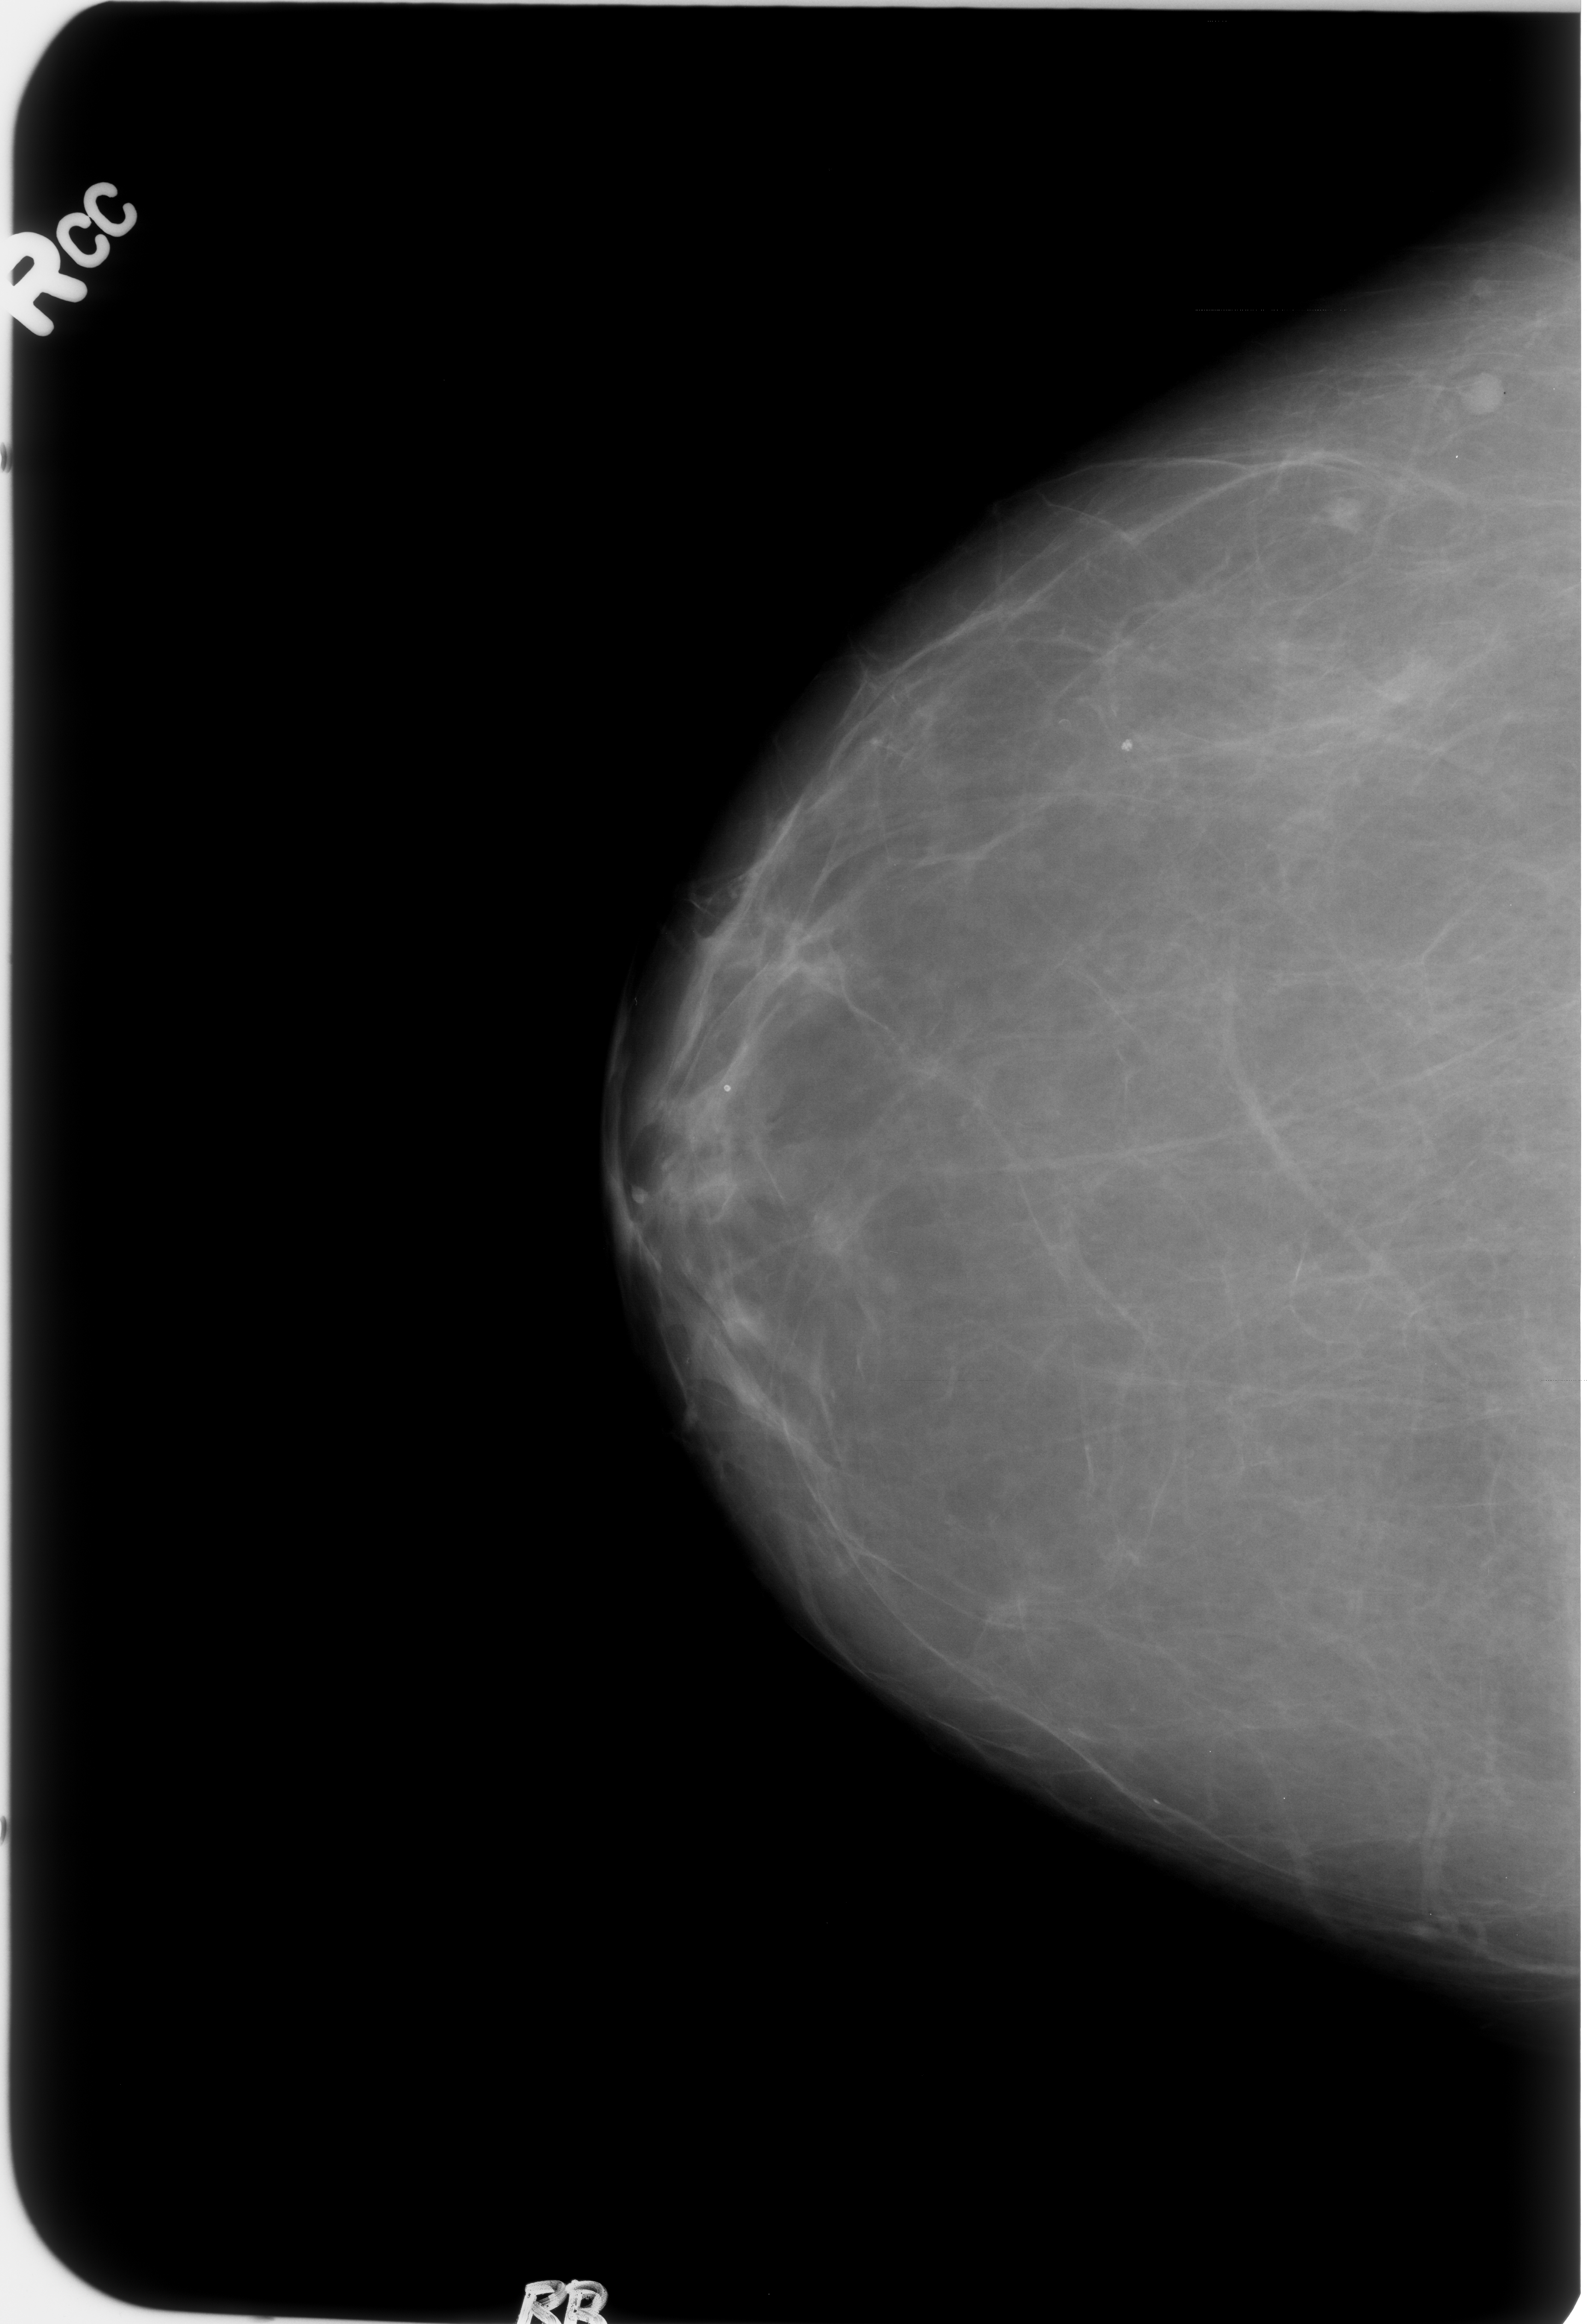
Digitized screen-film mammogram; right breast; CC view; BI-RADS breast density category 1 (scale 1–4); 1587 × 2324 image matrix.
Expert-marked regions of interest on this film, with their recorded descriptors:
- Finding 1 of 3: mass, shape lymph node, margins circumscribed; BI-RADS assessment category 2; subtlety rating 4 on a 1 (subtle) to 5 (obvious) scale; outcome (as recorded, no biopsy): benign without callback (not worked up further): box from (x=1108, y=722) to (x=1162, y=759) px
- Finding 2 of 3: mass, shape lymph node, margins circumscribed; BI-RADS assessment category 2; subtlety rating 4 on a 1 (subtle) to 5 (obvious) scale; outcome (as recorded, no biopsy): benign without callback (not worked up further): (x=1311, y=489)–(x=1366, y=537)
- Finding 3 of 3: mass, shape lymph node, margins circumscribed; BI-RADS assessment category 2; benign; no additional work-up was recommended (outcome (as recorded, no biopsy): benign without callback): (x=1456, y=372)–(x=1507, y=415)